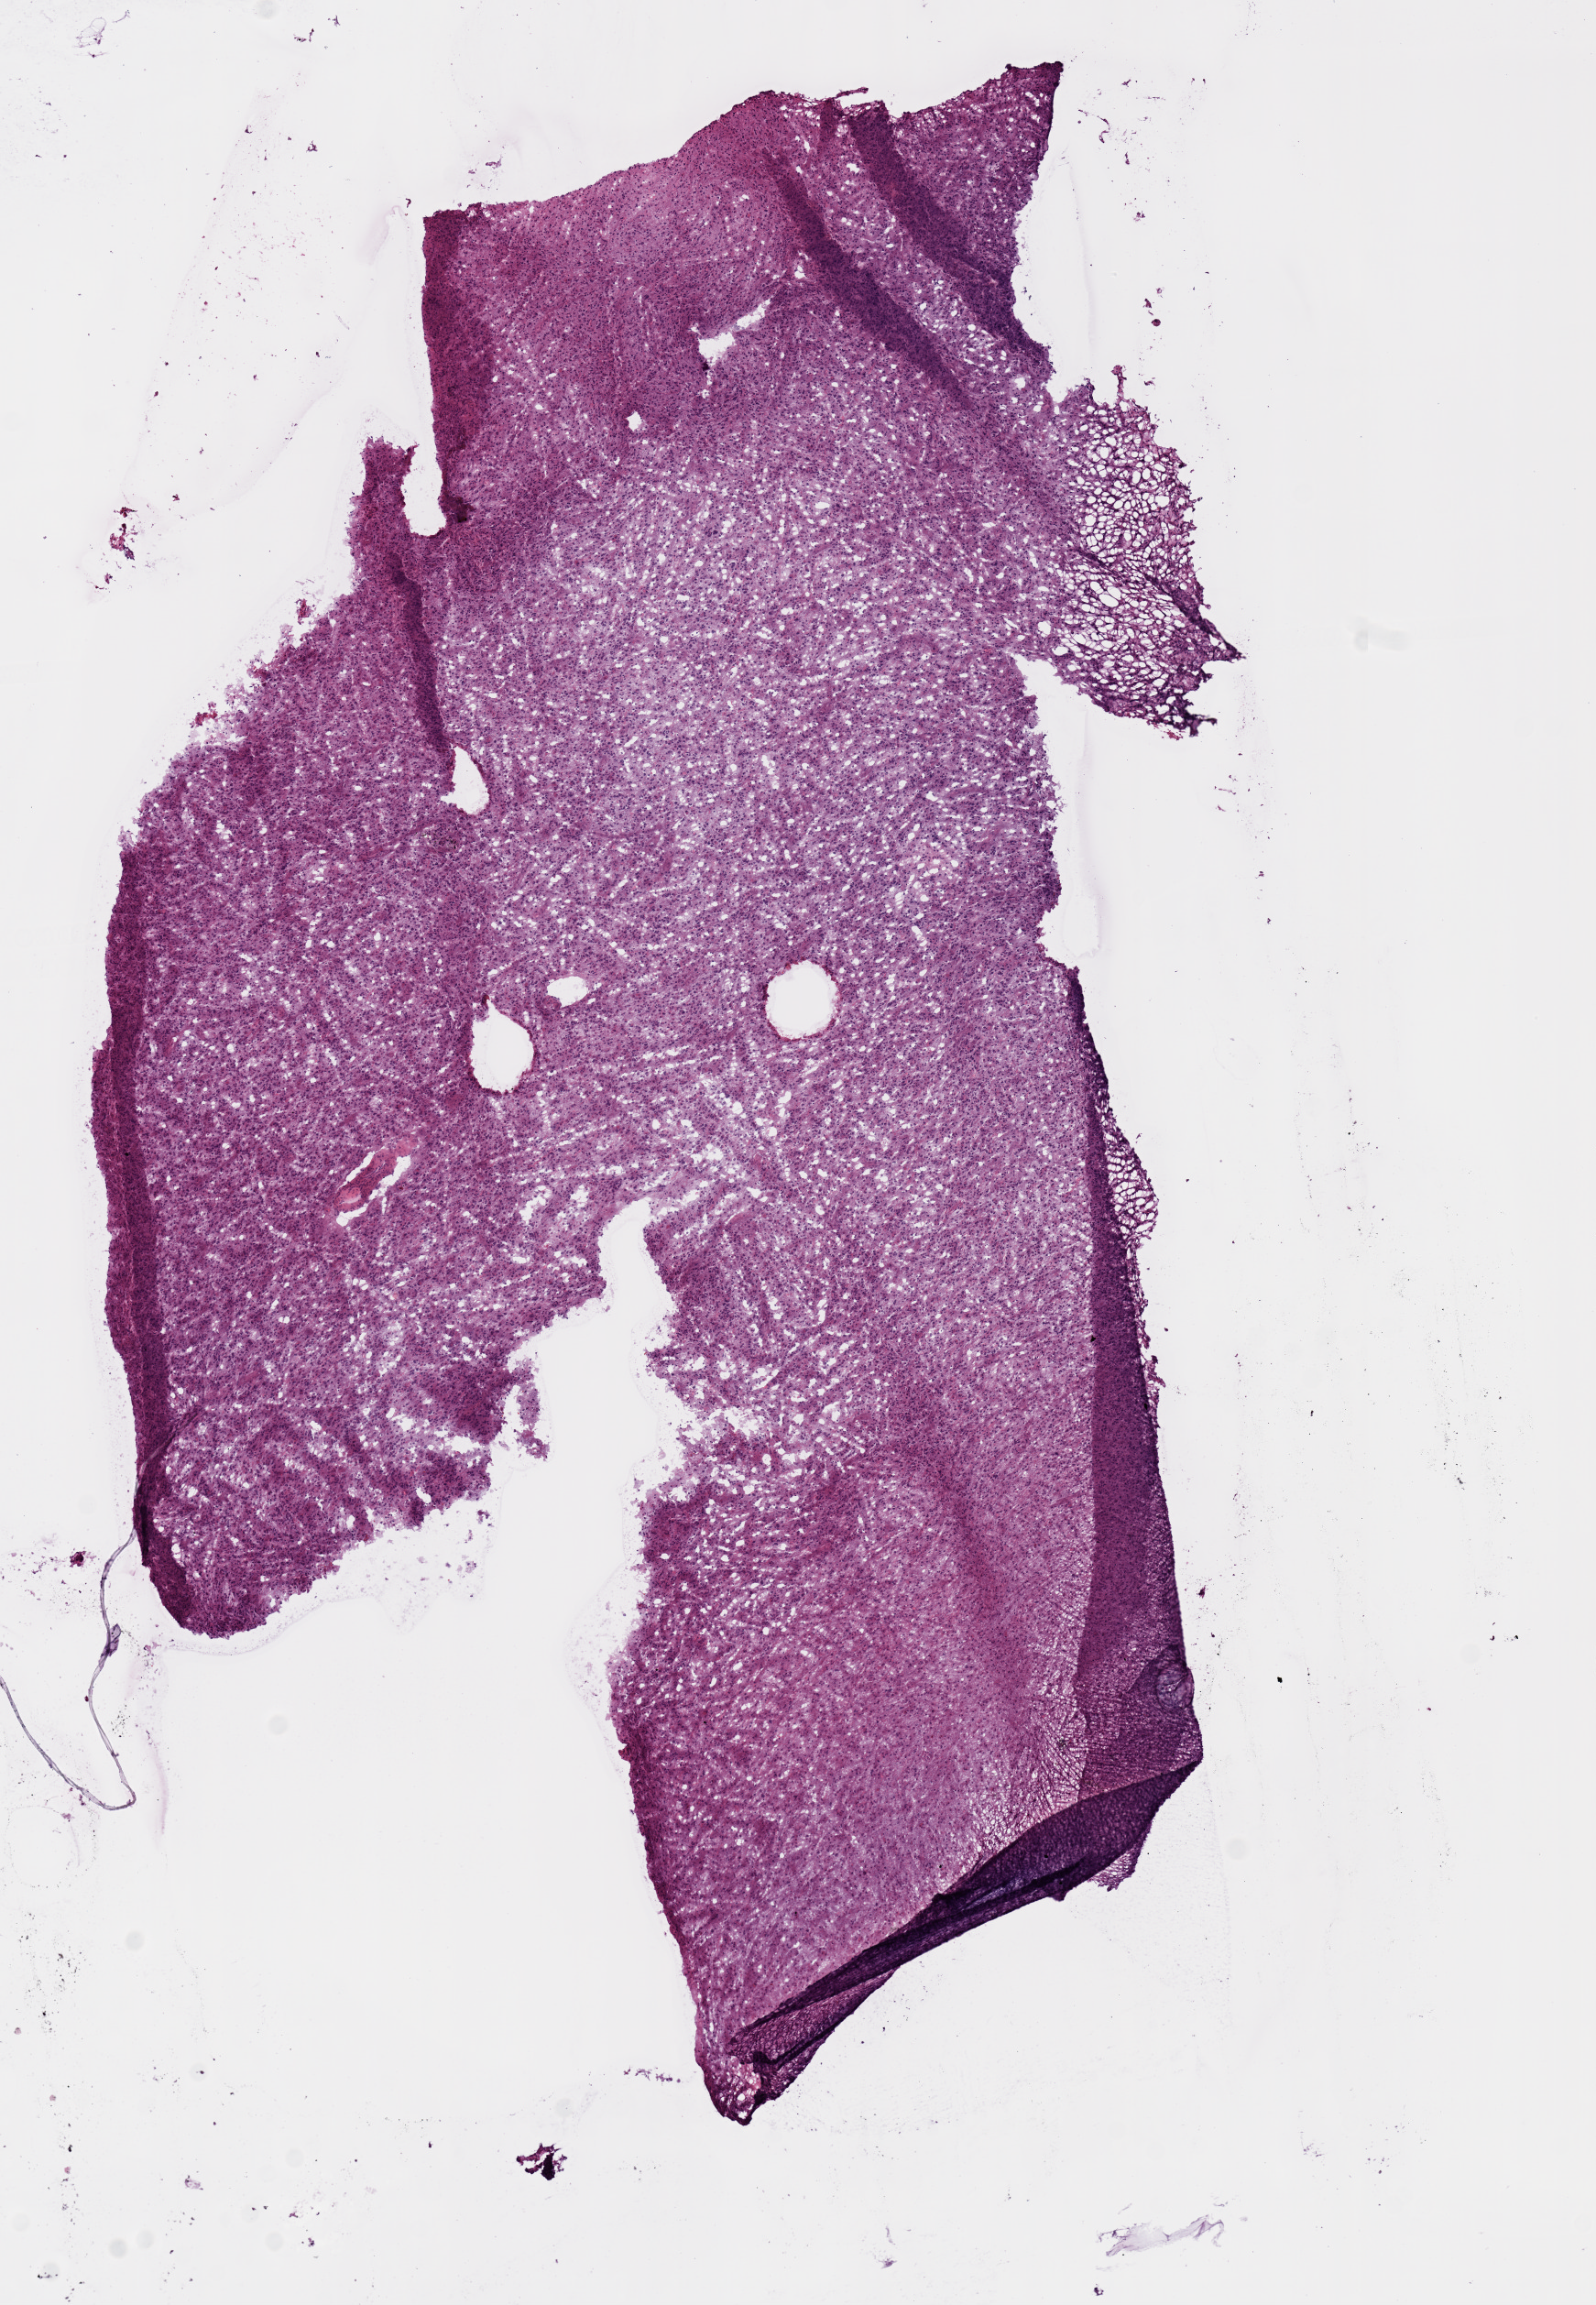
Digitized H&E tissue section (whole slide) — shown as a low-resolution overview of the whole scanned area (about 6.9 x 9.9 mm, from a 20x scan); frozen section from the top of the tissue portion; primary tumour sample from the brain. Patient: male, age at initial diagnosis 25 years. Histologic grade: G3 (poorly differentiated). Slide review estimates, as recorded: tumour cells 100%, tumour nuclei 75%, normal cells 0%, stromal cells 0%, necrosis 0%.
* laterality: midline
* diagnosis: Mixed glioma (cerebrum)